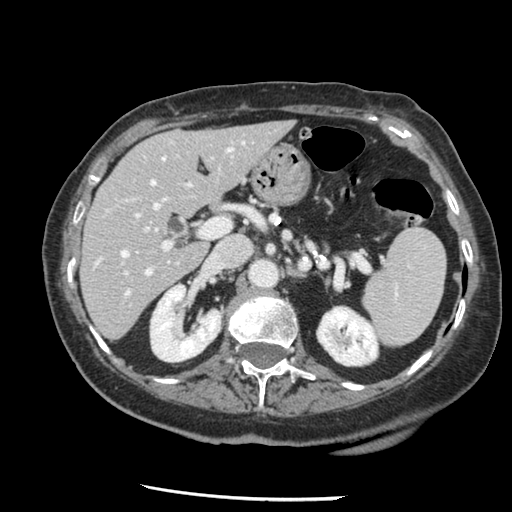
Contrast-enhanced abdominal CT, one axial slice. Position 78 of 148 along the scan axis. 120 kVp. Intravenous contrast given. Soft-tissue window (W 400 / L 40 HU). 2.5 mm slice thickness. 512 × 512 image matrix, field of view 330 × 330 mm. Female patient, age 85 years. Case-level facts recorded for this patient, not image findings: diagnosis: colorectal cancer liver metastases, imaged before liver resection; multiple liver metastases: no; largest metastasis: 0.9 cm; disease in both lobes: no.
Structures marked on this image (manually delineated by an expert):
- hepatic veins: box from (x=96, y=142) to (x=175, y=295) px
- liver: (x=82, y=122)–(x=292, y=339)
- planned liver remnant (the part of the liver to remain after resection): (x=82, y=122)–(x=292, y=339)
- portal vein (with intrahepatic branches): (x=124, y=145)–(x=230, y=276)